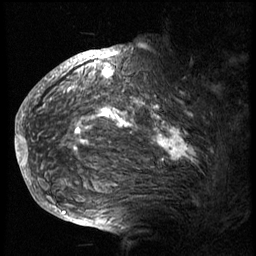
Breast MRI (dynamic contrast-enhanced), one sagittal slice. Position 51 of 74 along the scan axis. 3 images stored at this slice position (order not interpretable as contrast timing). 1.5 T. TE 4.2 ms, TR 8.9 ms. 2.5 mm slice thickness. 256 × 256 image matrix. Female patient, age 57 years. From the clinical record (not read from this slice): setting: breast cancer imaged before/during neoadjuvant chemotherapy; receptor status: HER2-positive.
Annotated regions visible in this slice (semi-automatic segmentation, software-assisted and operator-edited):
- analysis volume of interest (the breast-tissue region the enhancement analysis was run in; not a lesion): bounding box <40,62,240,175> (left, top, right, bottom; pixels)
- tumour enhancement mask (voxels above the 140 % enhancement threshold inside the analysis volume of interest): <40,62,194,163>